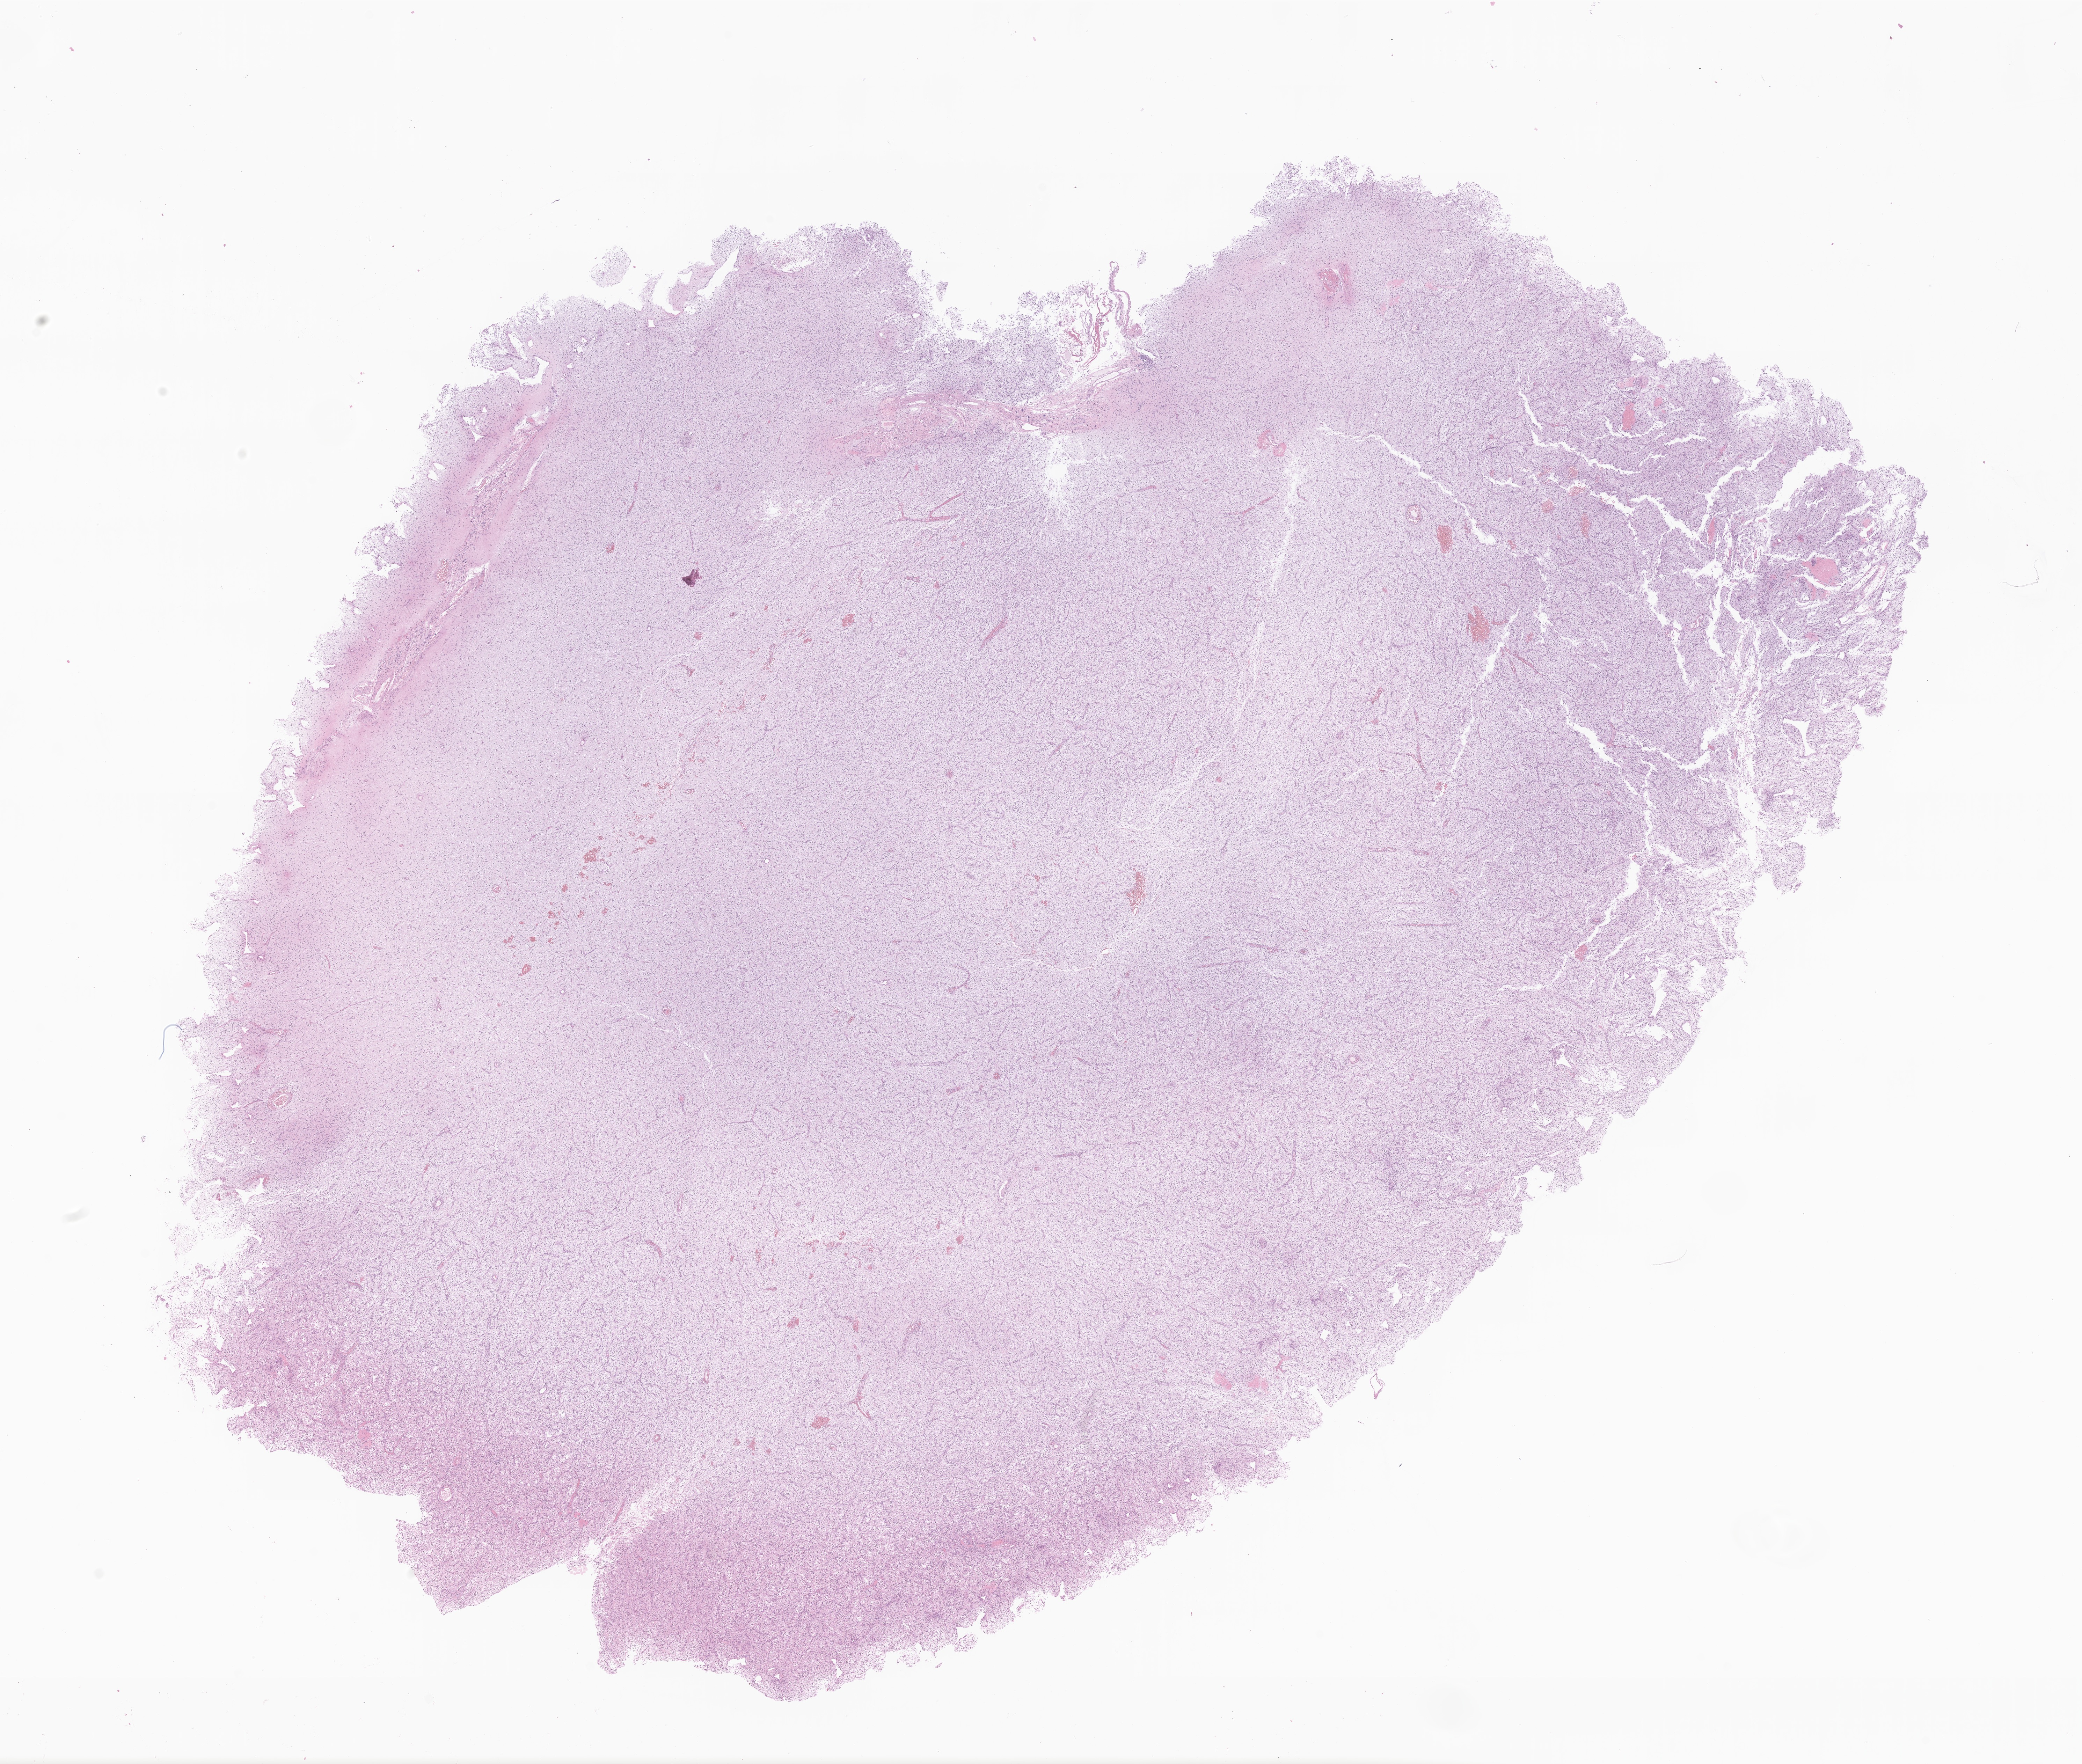
Whole-slide image, hematoxylin and eosin (H&E) stain of tumor tissue from the brain, a low-resolution overview of the entire scanned area, about 25.1 x 21.3 mm; FFPE section. Patient: male, age 52 months (4 years 4 months).
Diagnosis (ICD-O-3 morphology term): Astrocytoma, NOS.